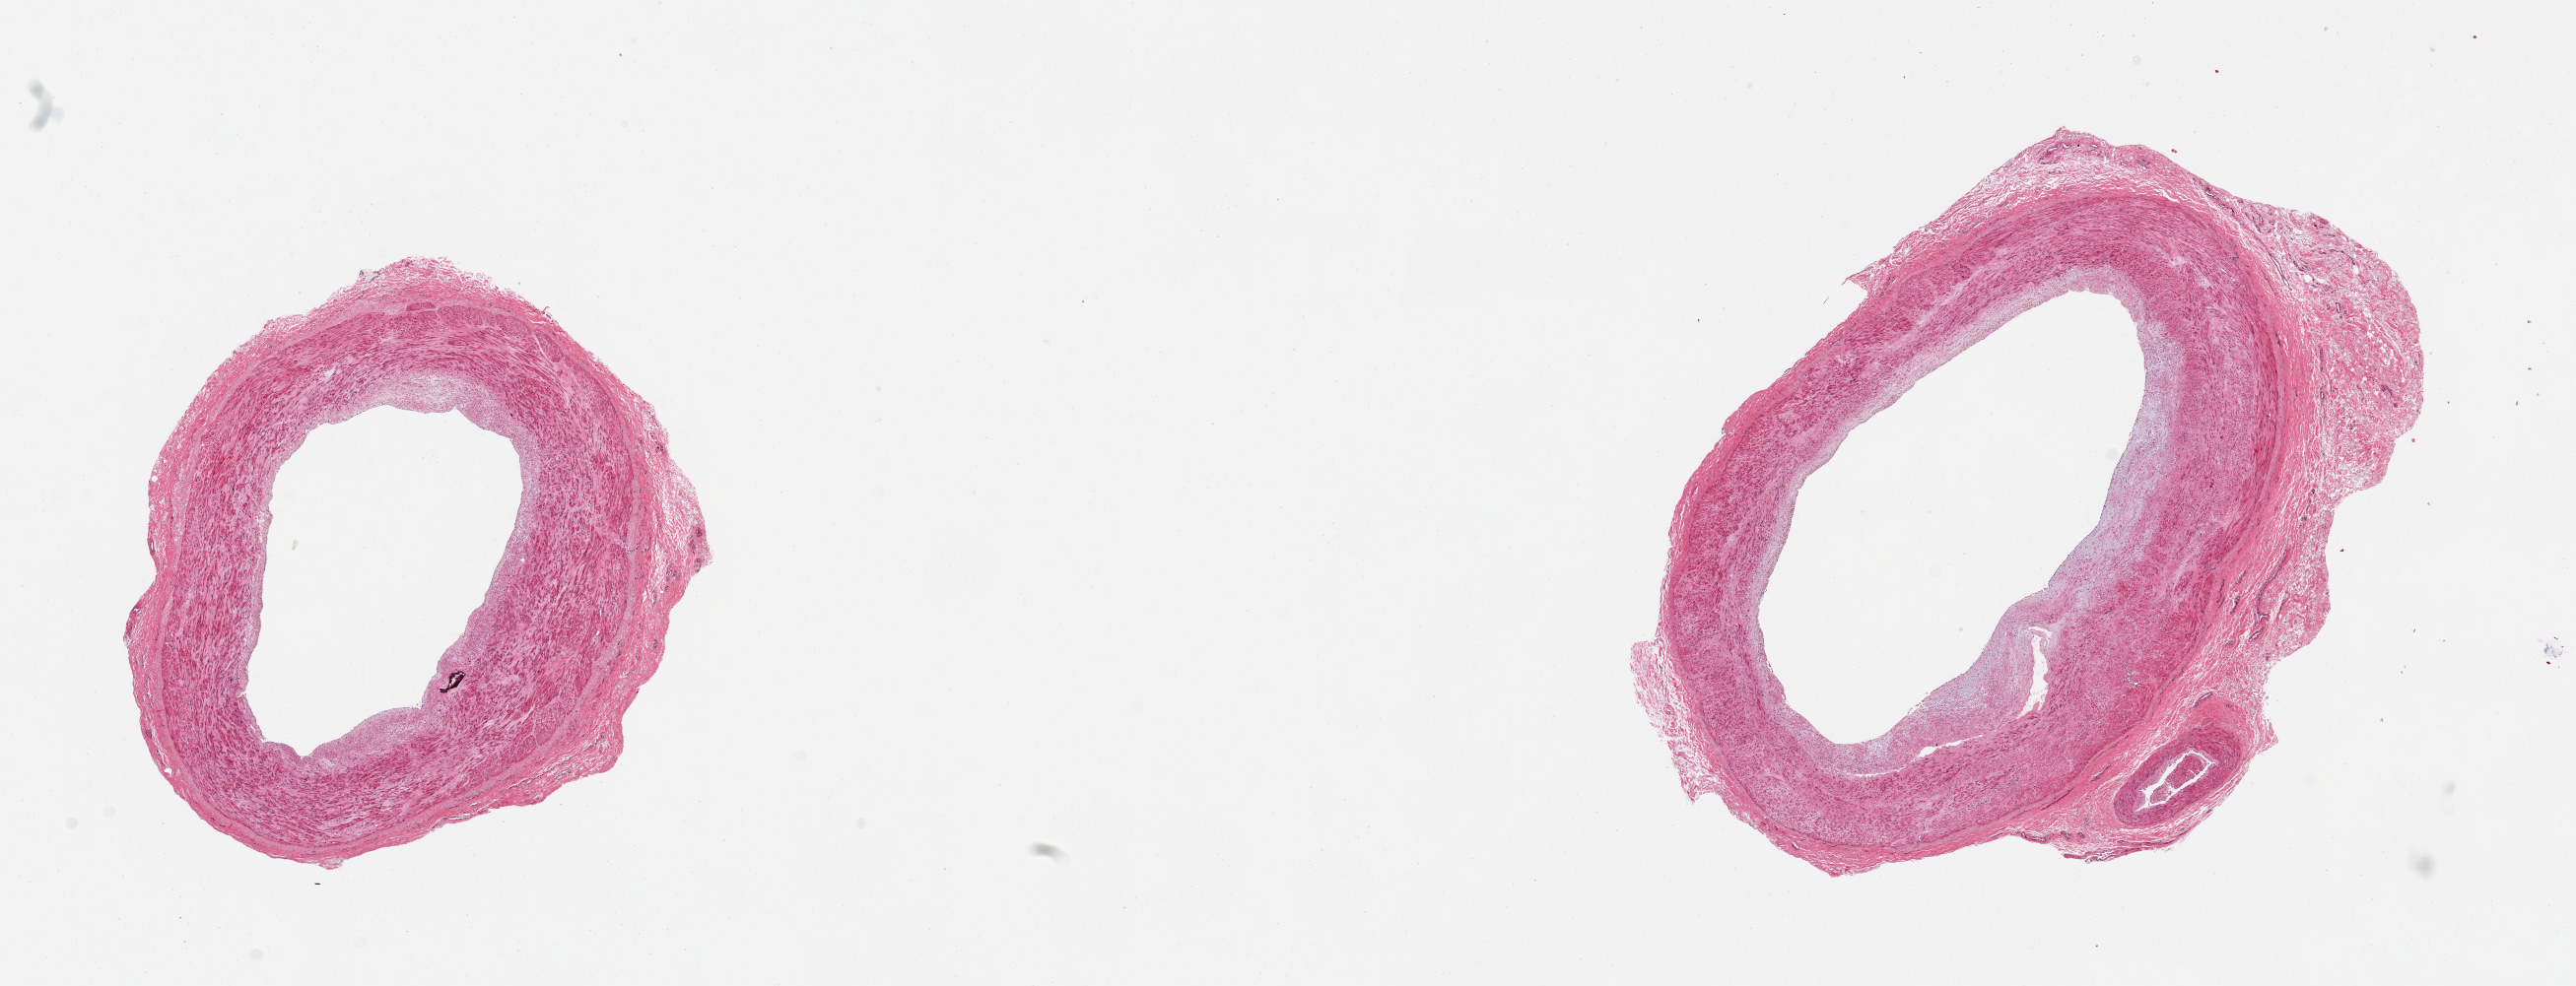
Hematoxylin and eosin (H&E) whole-slide image, low-resolution overview of the scanned area, about 20.7 x 7.9 mm, PAXgene-fixed, paraffin-embedded tissue, target tissue: tibial artery, donor tissue sample. Donor: male.
Review note (as recorded): 2 pieces. 5x5 & 7x5mm; Well trimmed, slight plaque, minute calcification.